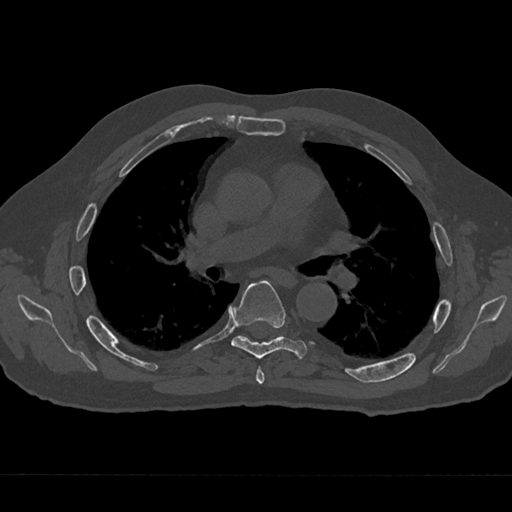
CT including the spine, one axial slice; 120 kVp; bone window (W 1800 / L 400 HU); 0.5 mm slice thickness; 512 × 512 image matrix, field of view 377 × 377 mm. Patient: male, 75 years. From the clinical record (not read from this slice): primary cancer: renal; vertebrae with lytic lesions (as recorded): T4.
Annotated regions visible in this slice (semi-automatic segmentation, software-assisted and operator-edited):
- T5 vertebra: bounding box <256,367,265,385> (left, top, right, bottom; pixels)
- T6 vertebra: <231,280,308,359>